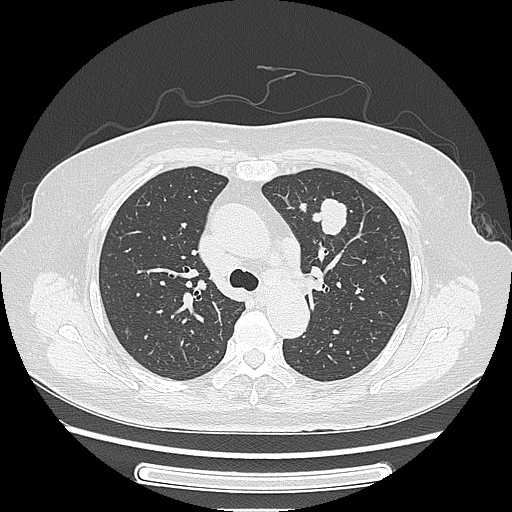
Chest CT, one axial slice. Position 165 of 227 along the scan axis. Reconstruction kernel LUNG. Lung window (W 1500 / L -600 HU). 1.25 mm slice thickness. 512 × 512 image matrix, field of view 363 × 363 mm. Patient: female, 77 years. From the clinical record (not read from this slice): clinical TNM (as recorded): T1c N3 M0; histopathological grade: G2-3.
Outlined on this slice (rectangle marked by the reading radiologist):
- lung tumour (recorded histology: adenocarcinoma): bounding box [x1, y1, x2, y2] px = [311, 191, 354, 244]